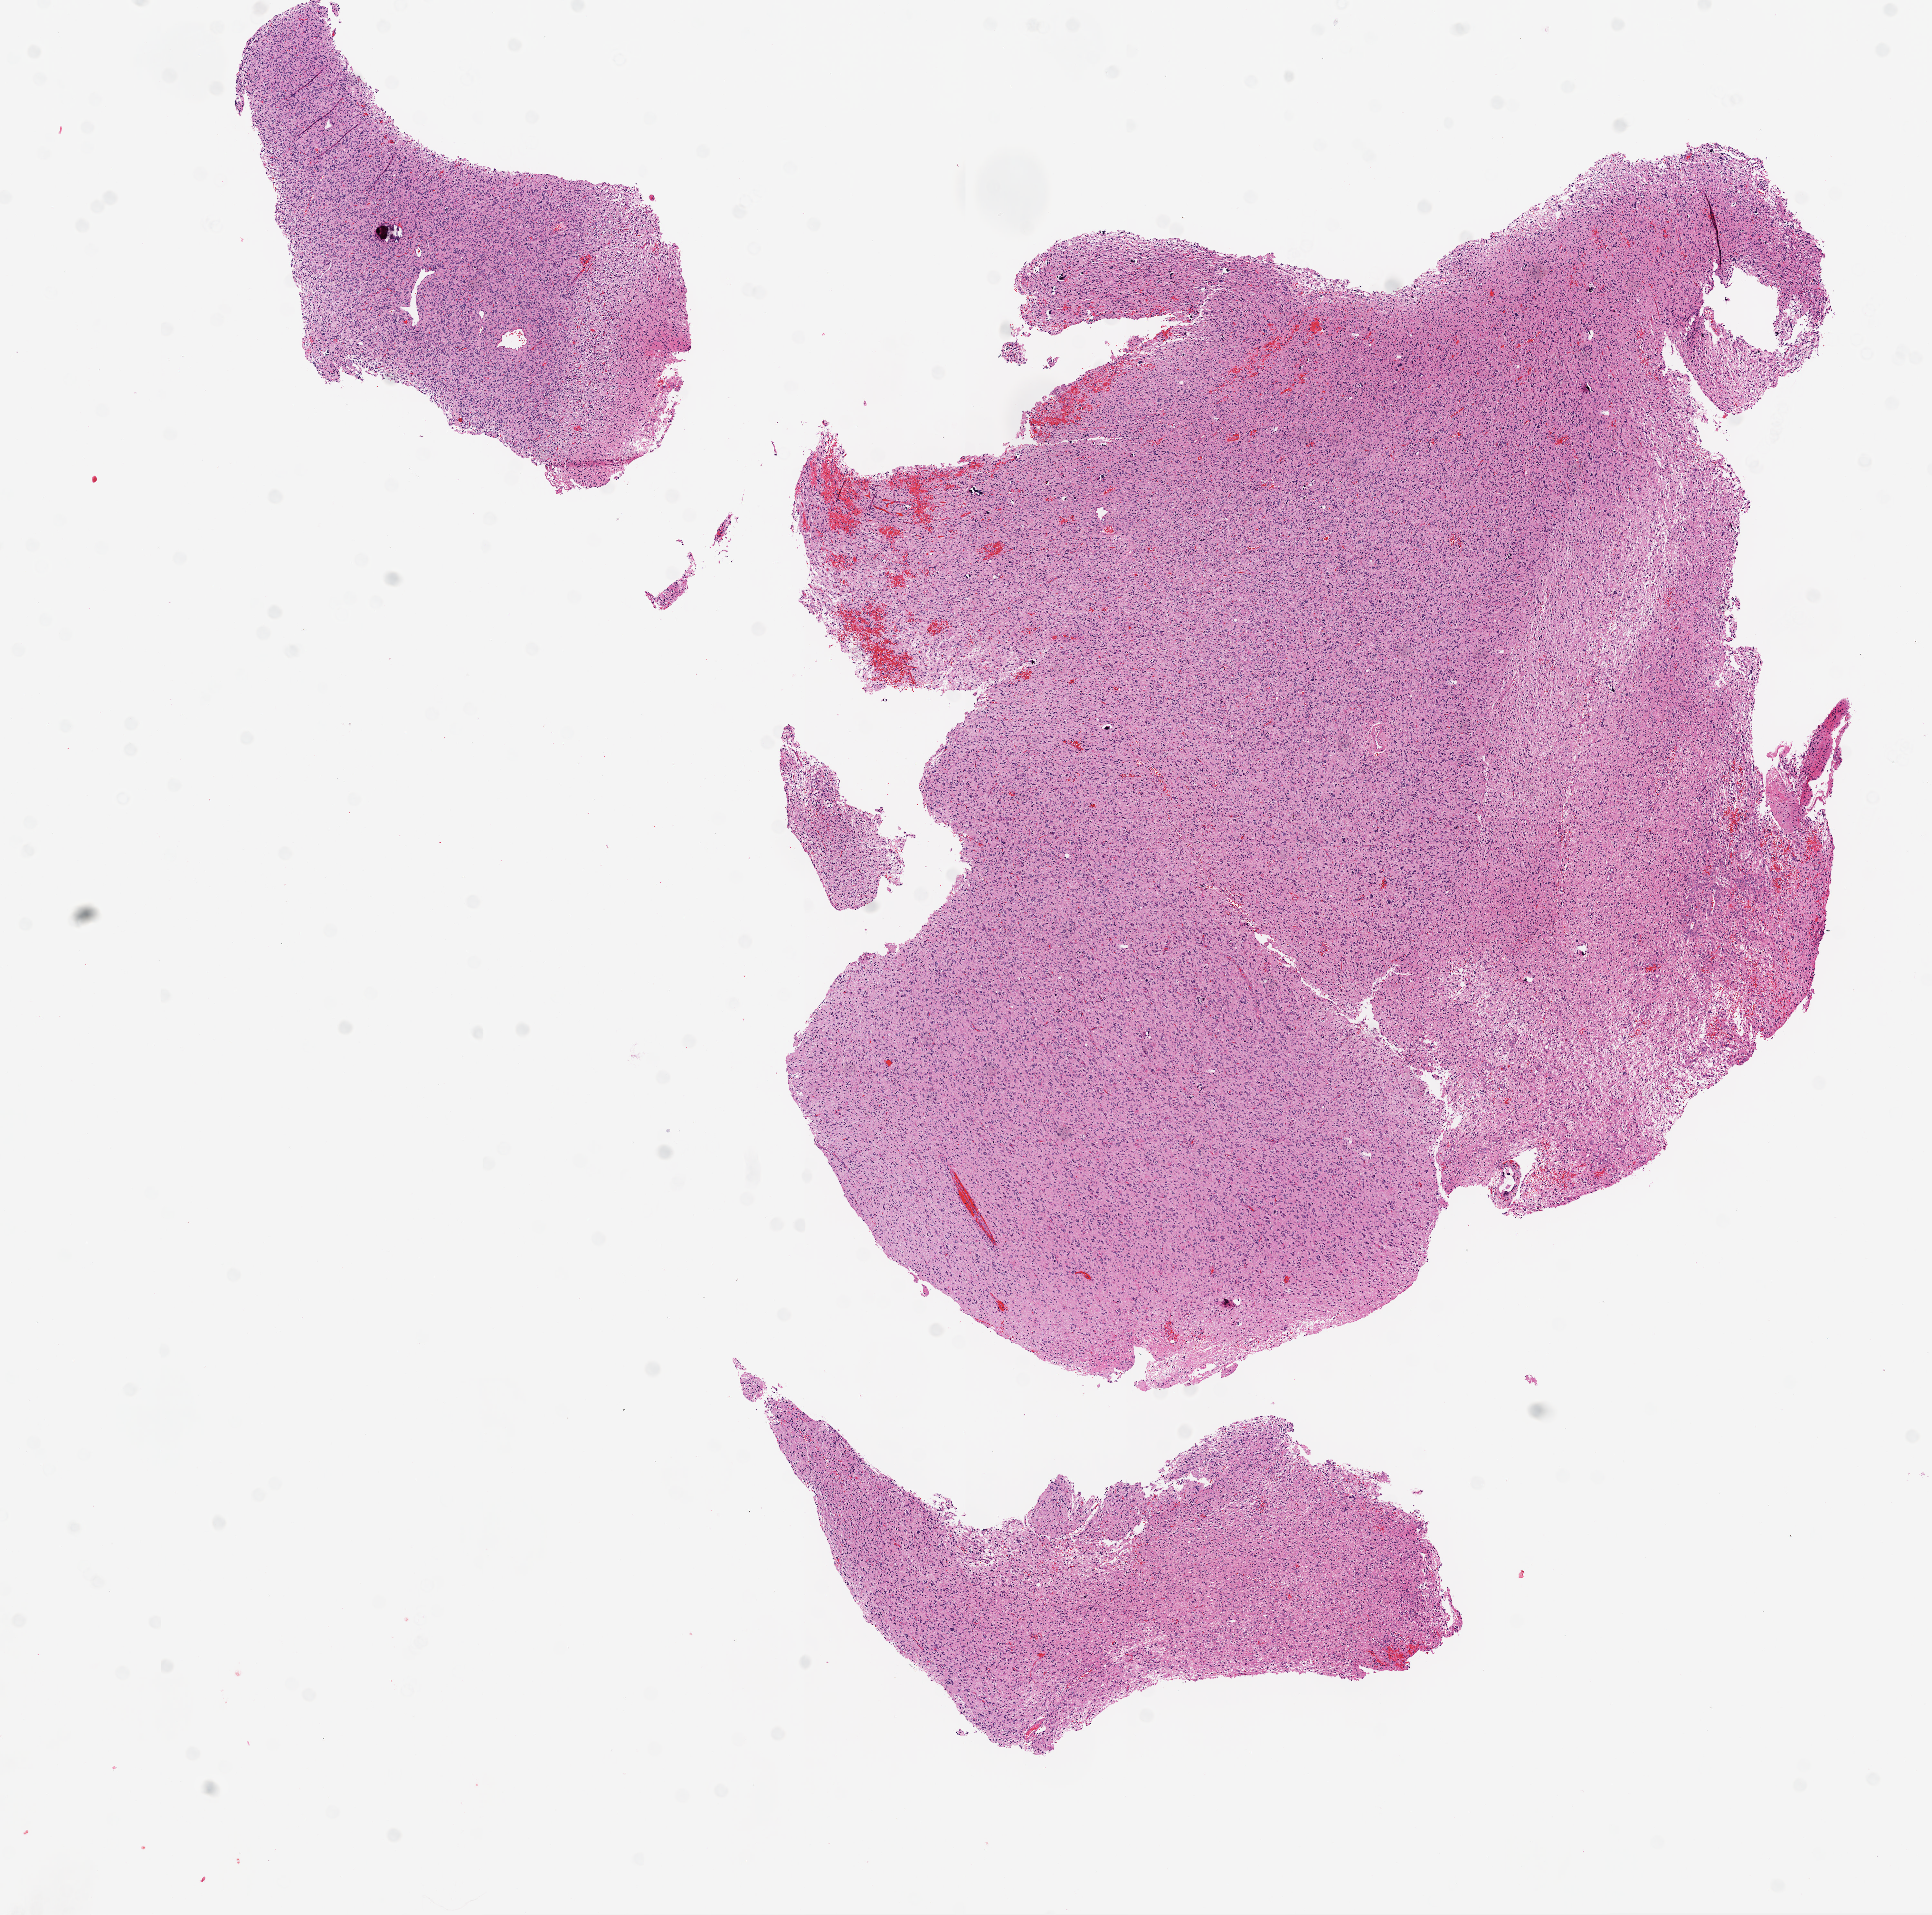
Whole-slide histology image, Hematoxylin and eosin (H&E) stained — low-resolution overview of the scanned area, about 12.0 x 11.9 mm (acquisition: 20x scan), frozen section from the top of the tissue portion, primary tumour sample from the brain. Patient: male, age at initial diagnosis 71 years. Composition of this section per pathologist review: tumour cells 100%, tumour nuclei 75%, normal cells 0%, stromal cells 0%, necrosis 0%.
Histologic diagnosis: Glioblastoma.